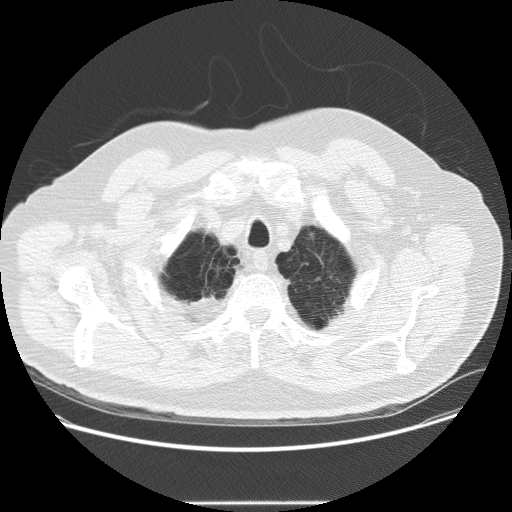
Chest CT (low-dose screening protocol), one axial image. Second annual screen. Lung window (W 1500 / L -600 HU). Standard (soft-tissue) reconstruction kernel (STANDARD). Male participant, aged 64 years at enrolment.
Expert reader's lesion annotation, bounding box (x1, y1, x2, y2) in pixels: (300, 224, 326, 250). Reader record for this screening exam (exam-level; its link to the box is not recorded): non-calcified nodule or mass ≥4 mm, left upper lobe, 5 × 3 mm, smooth margins, soft tissue attenuation, pre-existing on the prior screen: no. Official screen result: positive, other. Lung cancer was diagnosed 300 days after this screen: adenocarcinoma, NOS, left upper lobe, poorly differentiated (G3), stage IA (AJCC 6th edition), 8 mm at pathology.